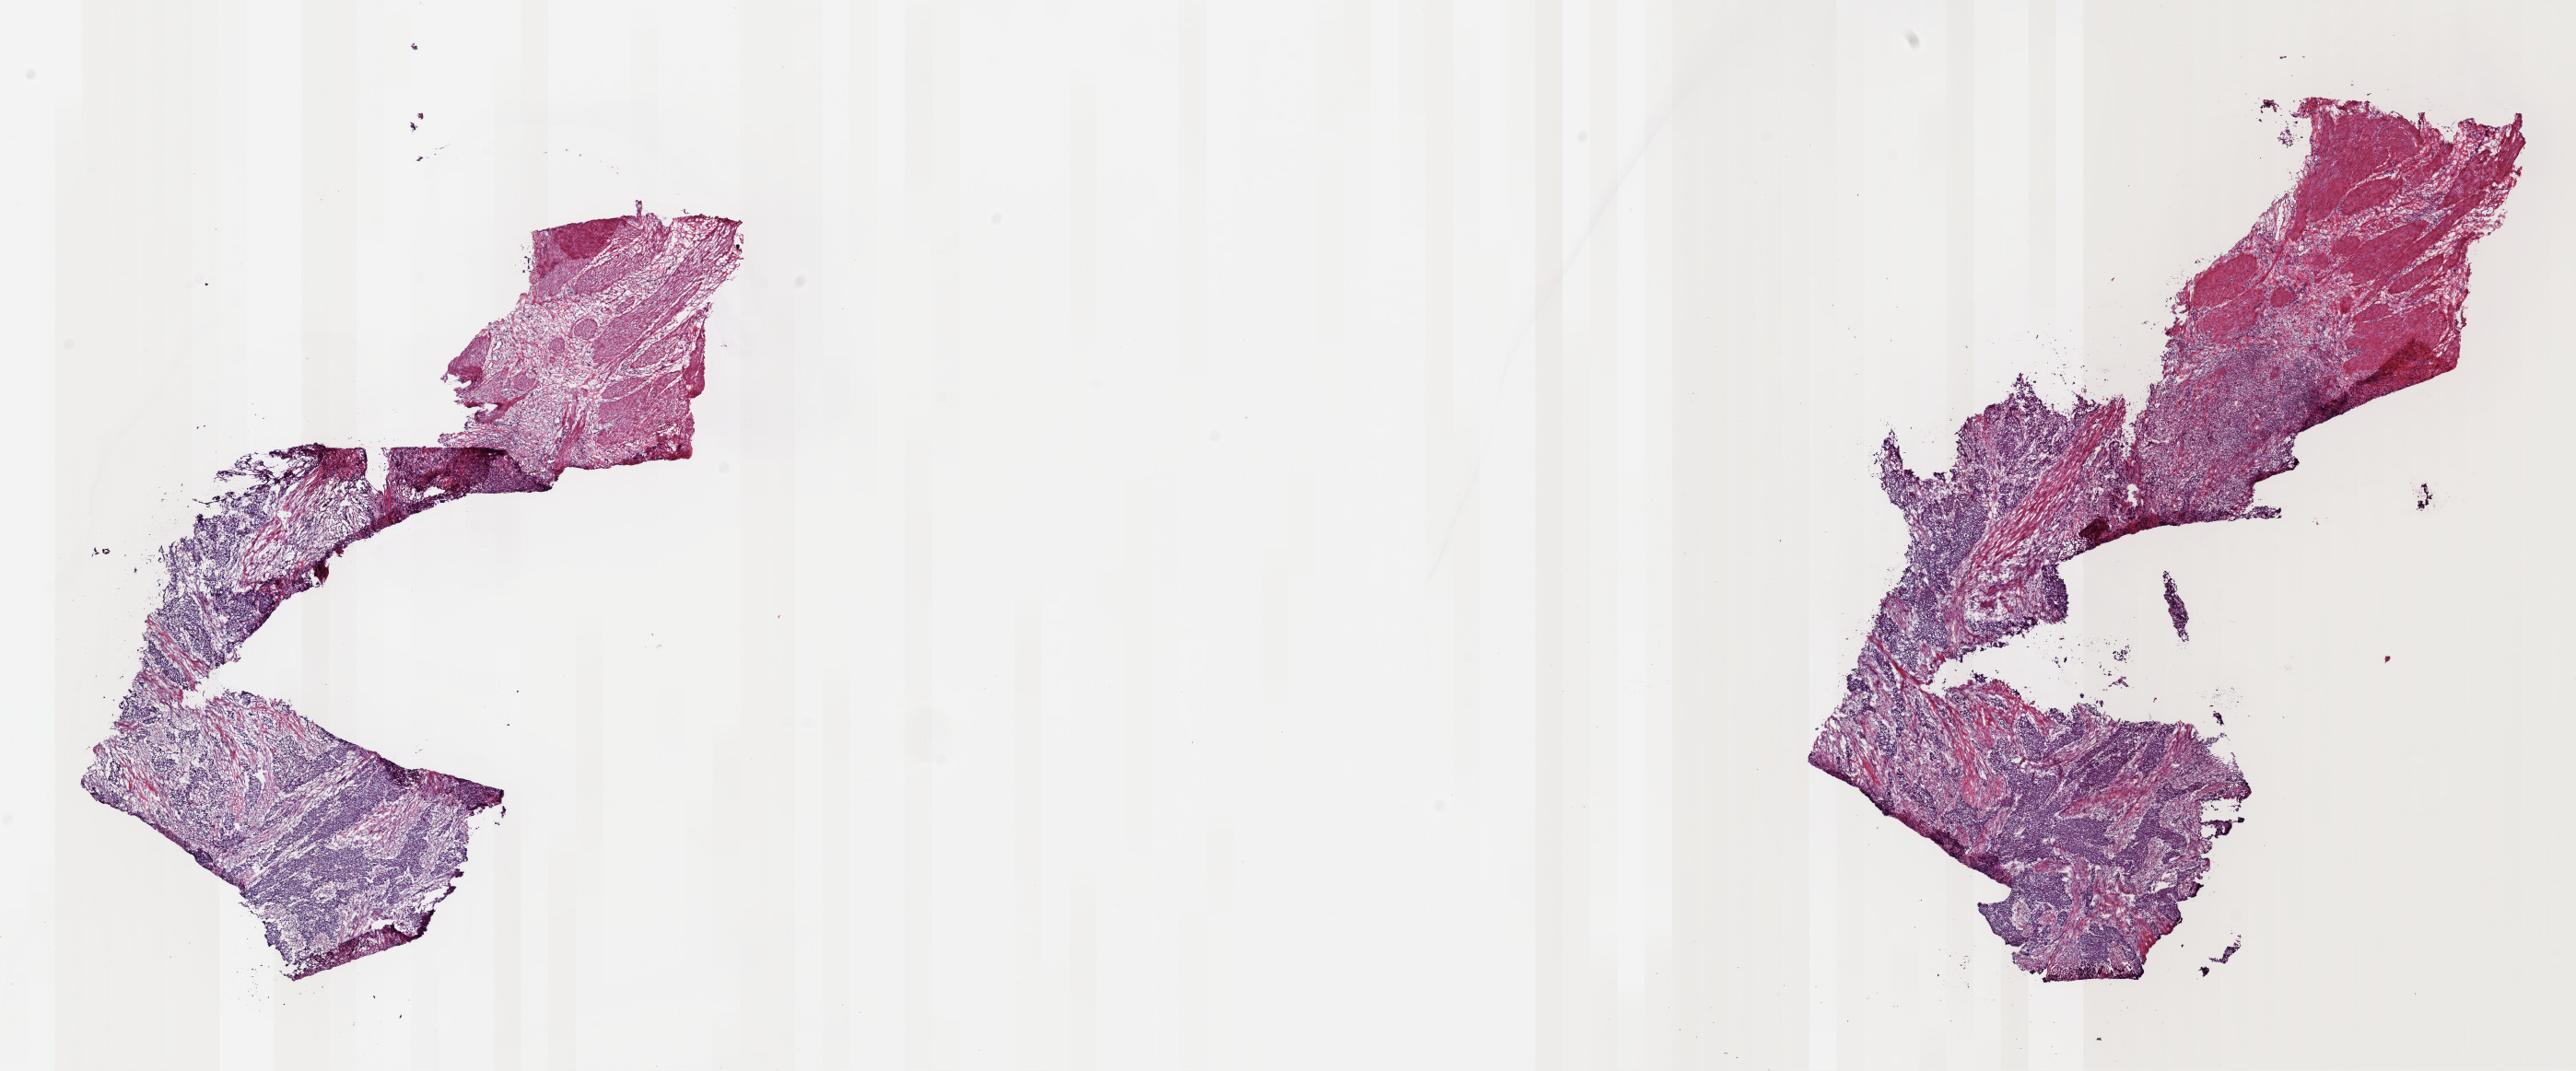
H&E whole-slide image — low-resolution overview of the scanned area, about 22.1 x 9.2 mm (slide scanned at 40x), frozen section, primary tumour sample from the bladder. Patient: male, age at initial diagnosis 56 years. Histologic grade: high grade. Composition of this section per pathologist review: tumour cells 70%, tumour nuclei 85%, normal cells 30%, stromal cells 0%, necrosis 0%. Infiltration values recorded for this section: lymphocyte infiltration 0%, monocyte infiltration 0%, neutrophil infiltration 0%.
Lymph nodes positive (case pathology): 0 of 25 examined. Diagnosis: Transitional cell carcinoma. AJCC pathologic stage: II.